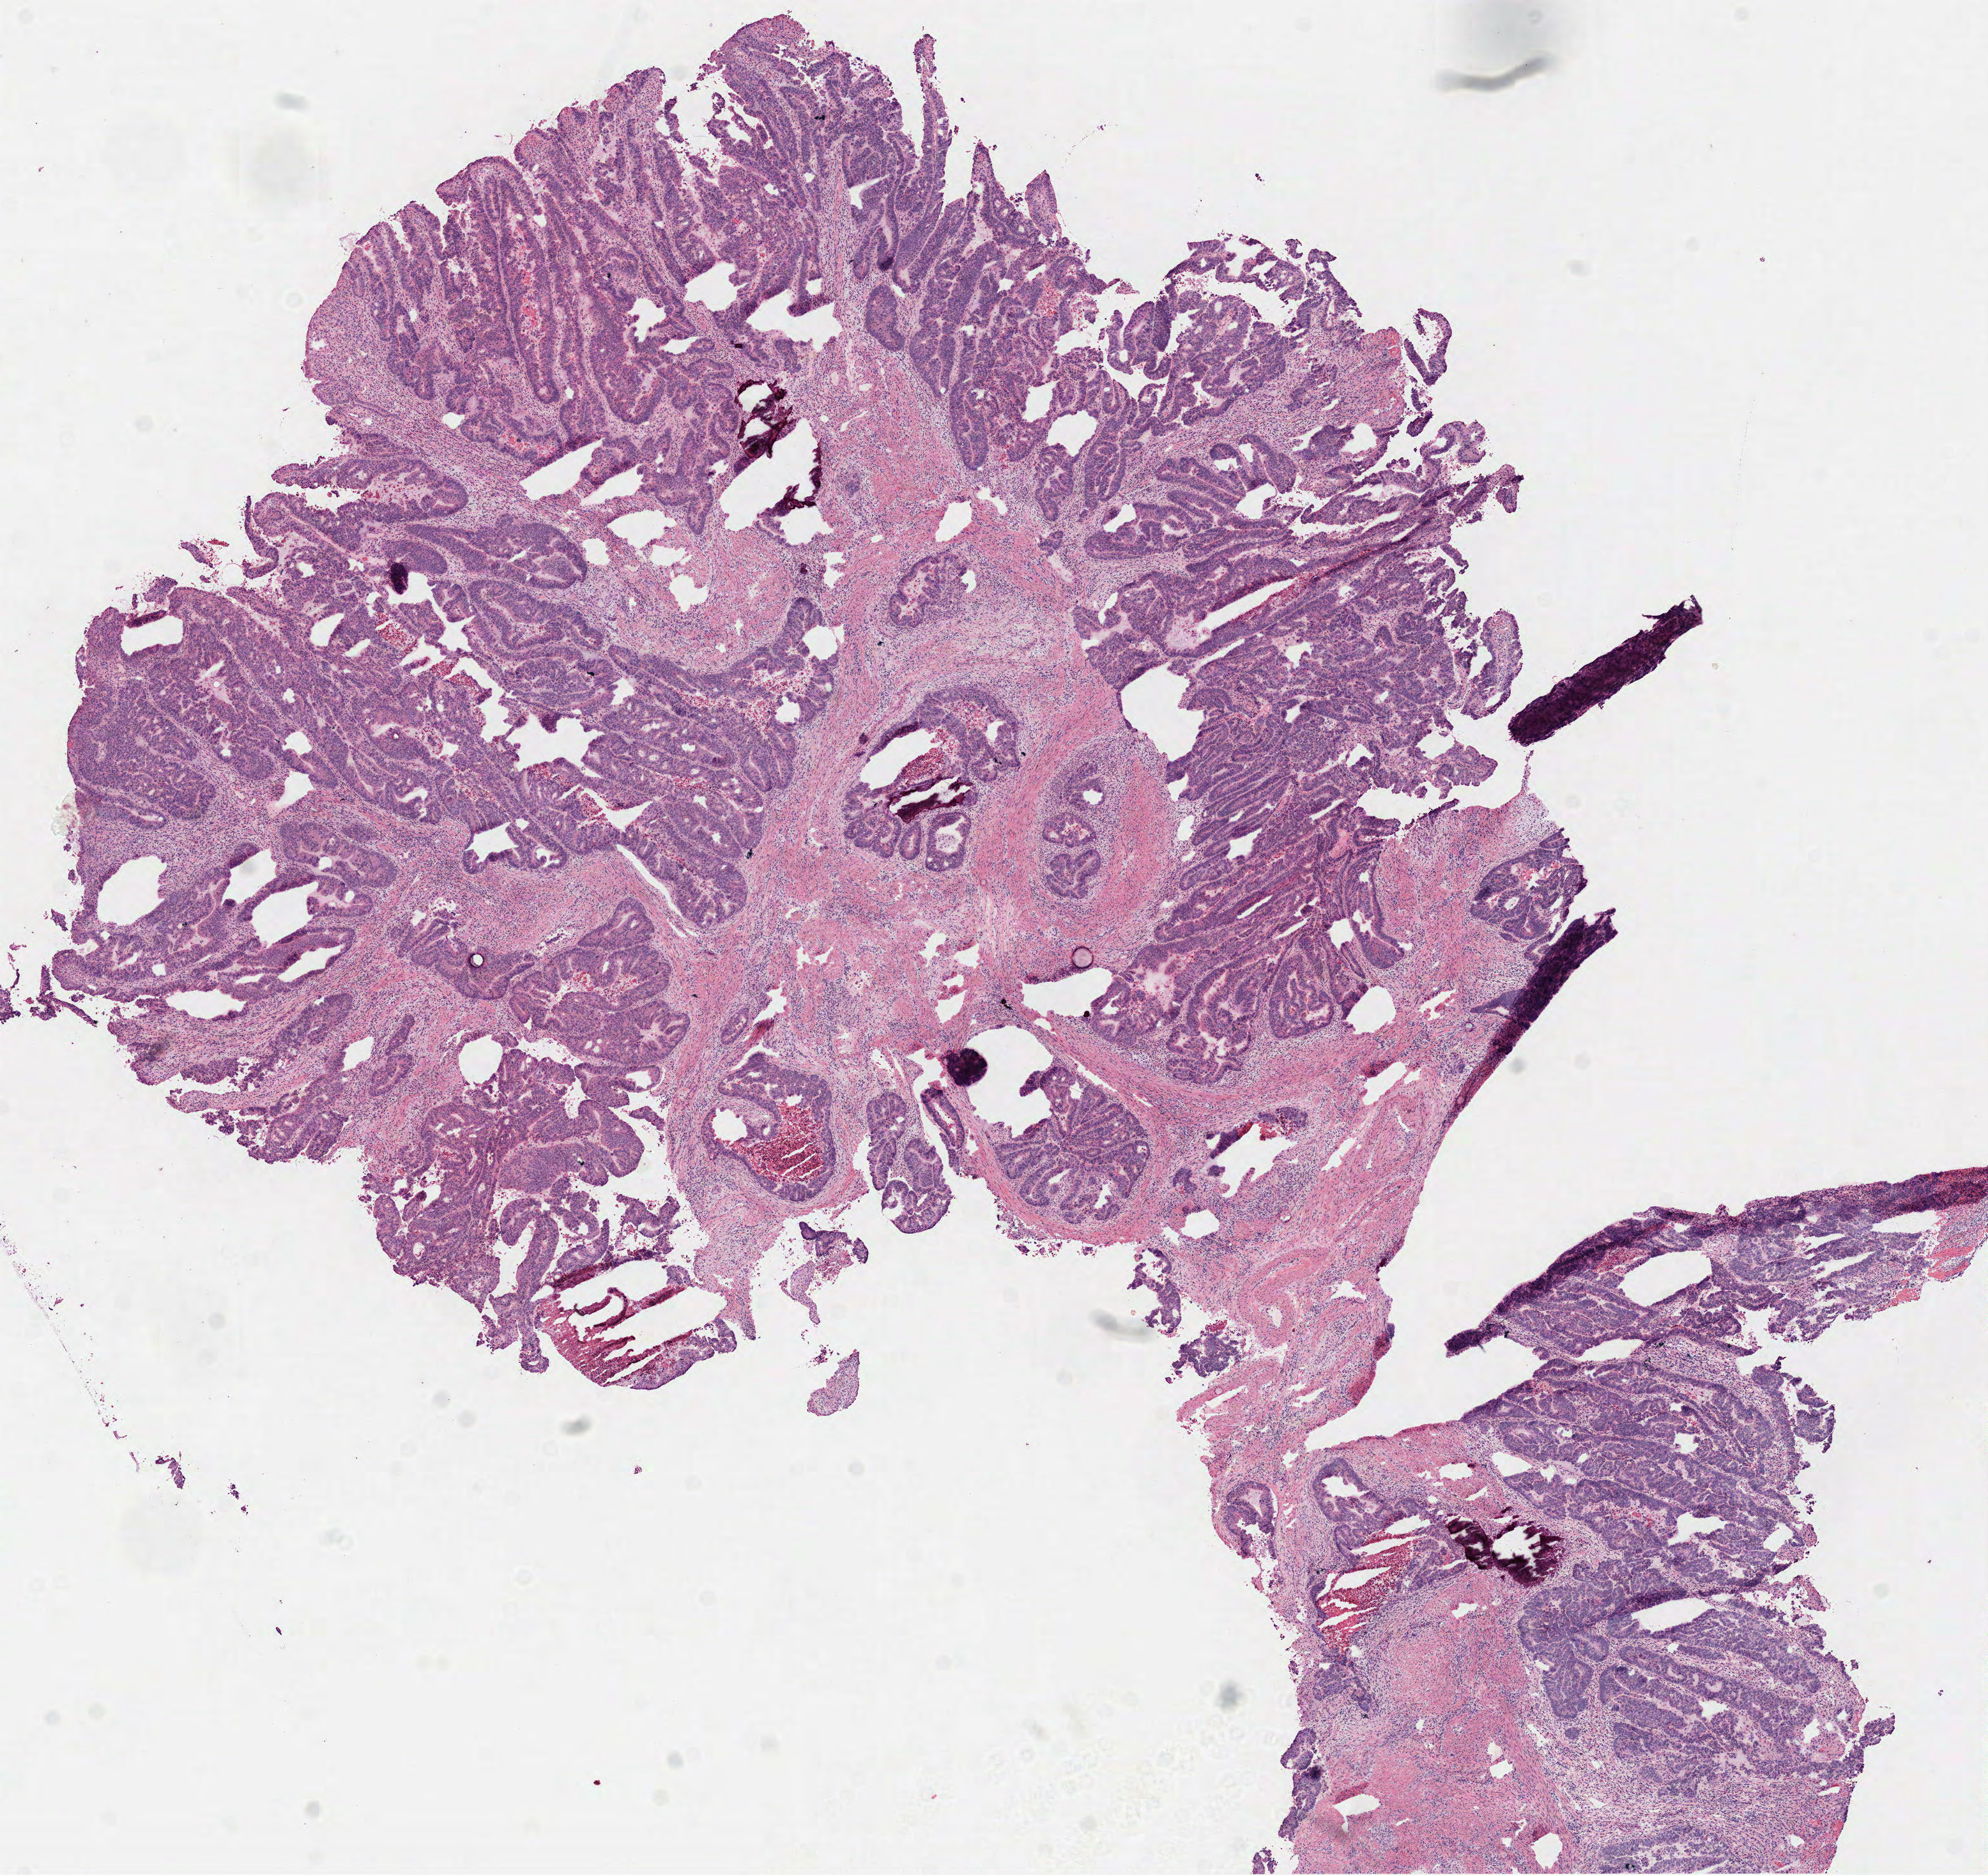
Whole-slide histology image, H&E-stained — low-resolution overview of the scanned area, about 12.5 x 11.8 mm (from a 40x scan). Frozen section from the top of the tissue portion. Sample: primary tumour, colon. Patient: male, age at initial diagnosis 82 years. Slide review estimates, as recorded: tumour cells 70%, tumour nuclei 75%, normal cells 0%, stromal cells 20%, necrosis 10%.
* AJCC pathologic stage: I (7th edition)
* pathologic diagnosis: Adenocarcinoma, NOS (sigmoid colon)
* lymph nodes positive (case pathology): 0 of 17 examined